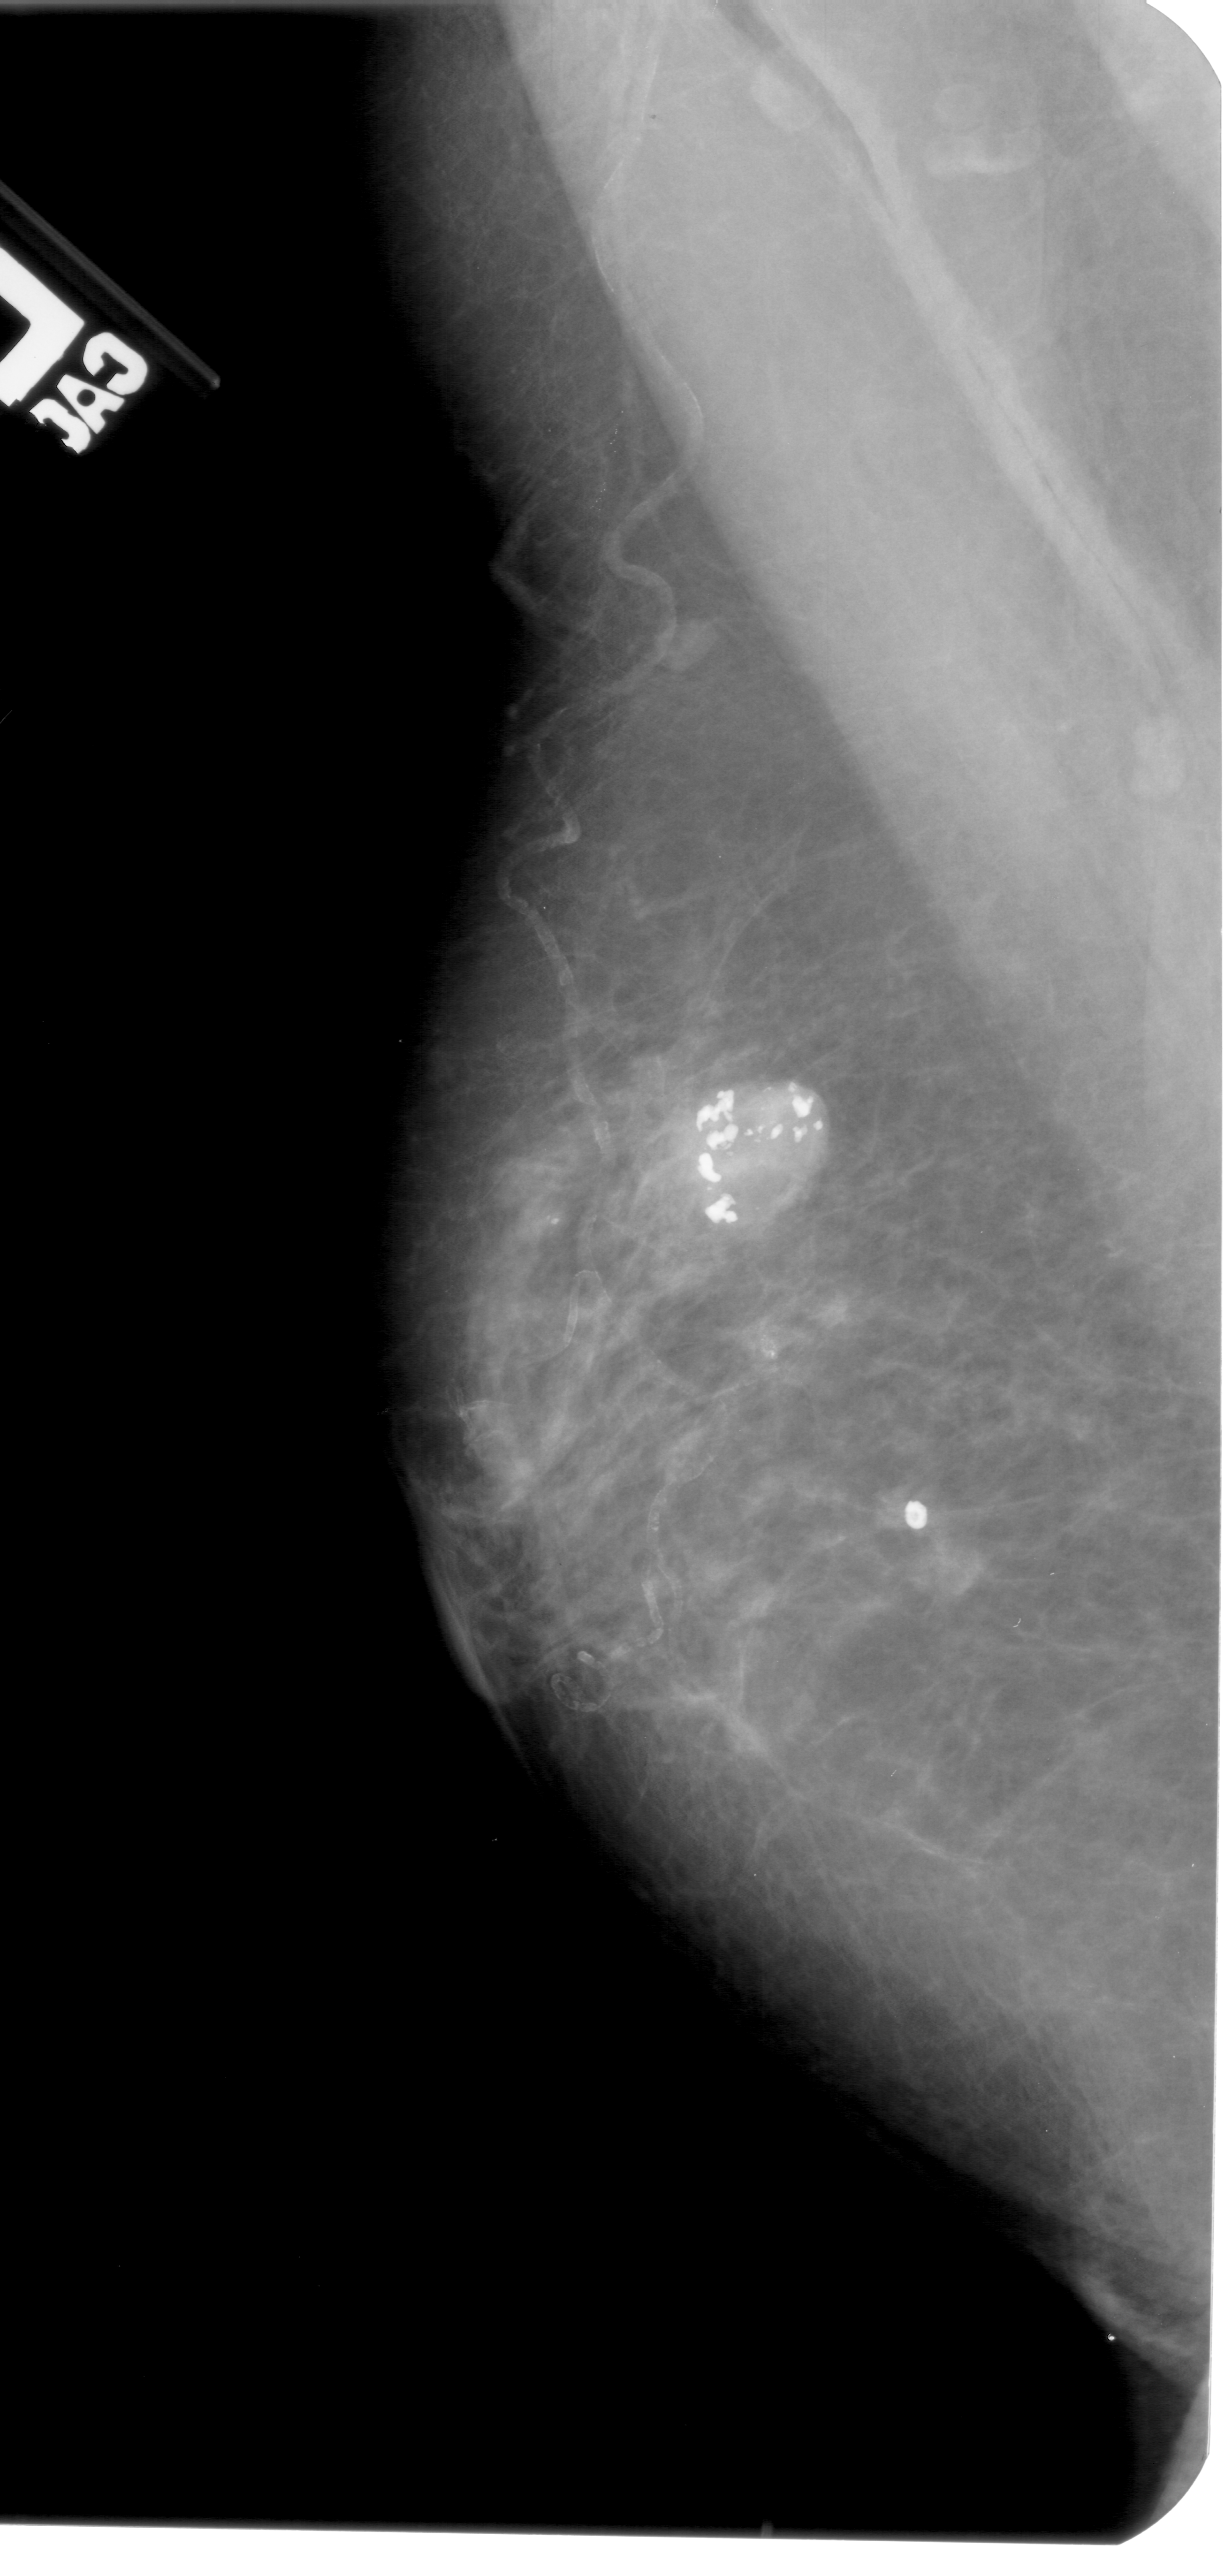
Mammogram (digitized film), left breast, mediolateral oblique (MLO) view, BI-RADS breast density category 3 (scale 1–4).
- Marked abnormality: calcifications, morphology amorphous; BI-RADS assessment category 2; pathology result (as recorded, not read from the image): benign.